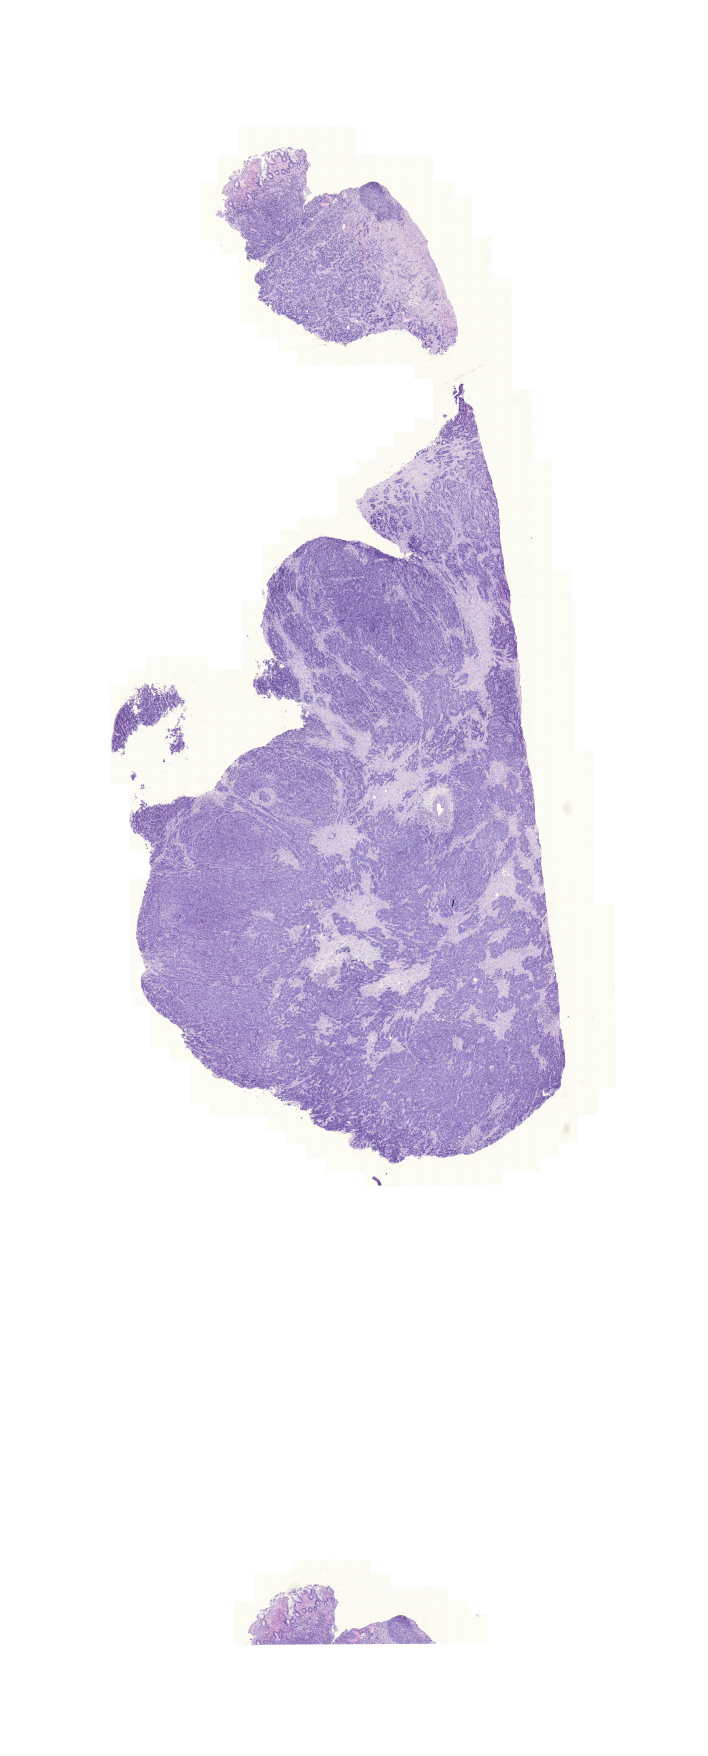
Digitized H&E-stained tissue section (whole slide), a low-resolution overview of the entire scanned area, about 10.5 x 26.1 mm (from a 20x scan). Formalin-fixed paraffin-embedded (FFPE) diagnostic section. Colon, primary tumour sample. Female patient; age at initial diagnosis 84 years.
- TNM: T3 N0 M0
- diagnosis: Adenocarcinoma, NOS
- AJCC pathologic stage: IIA (6th edition)
- lymph nodes positive (case pathology): 0 of 18 examined